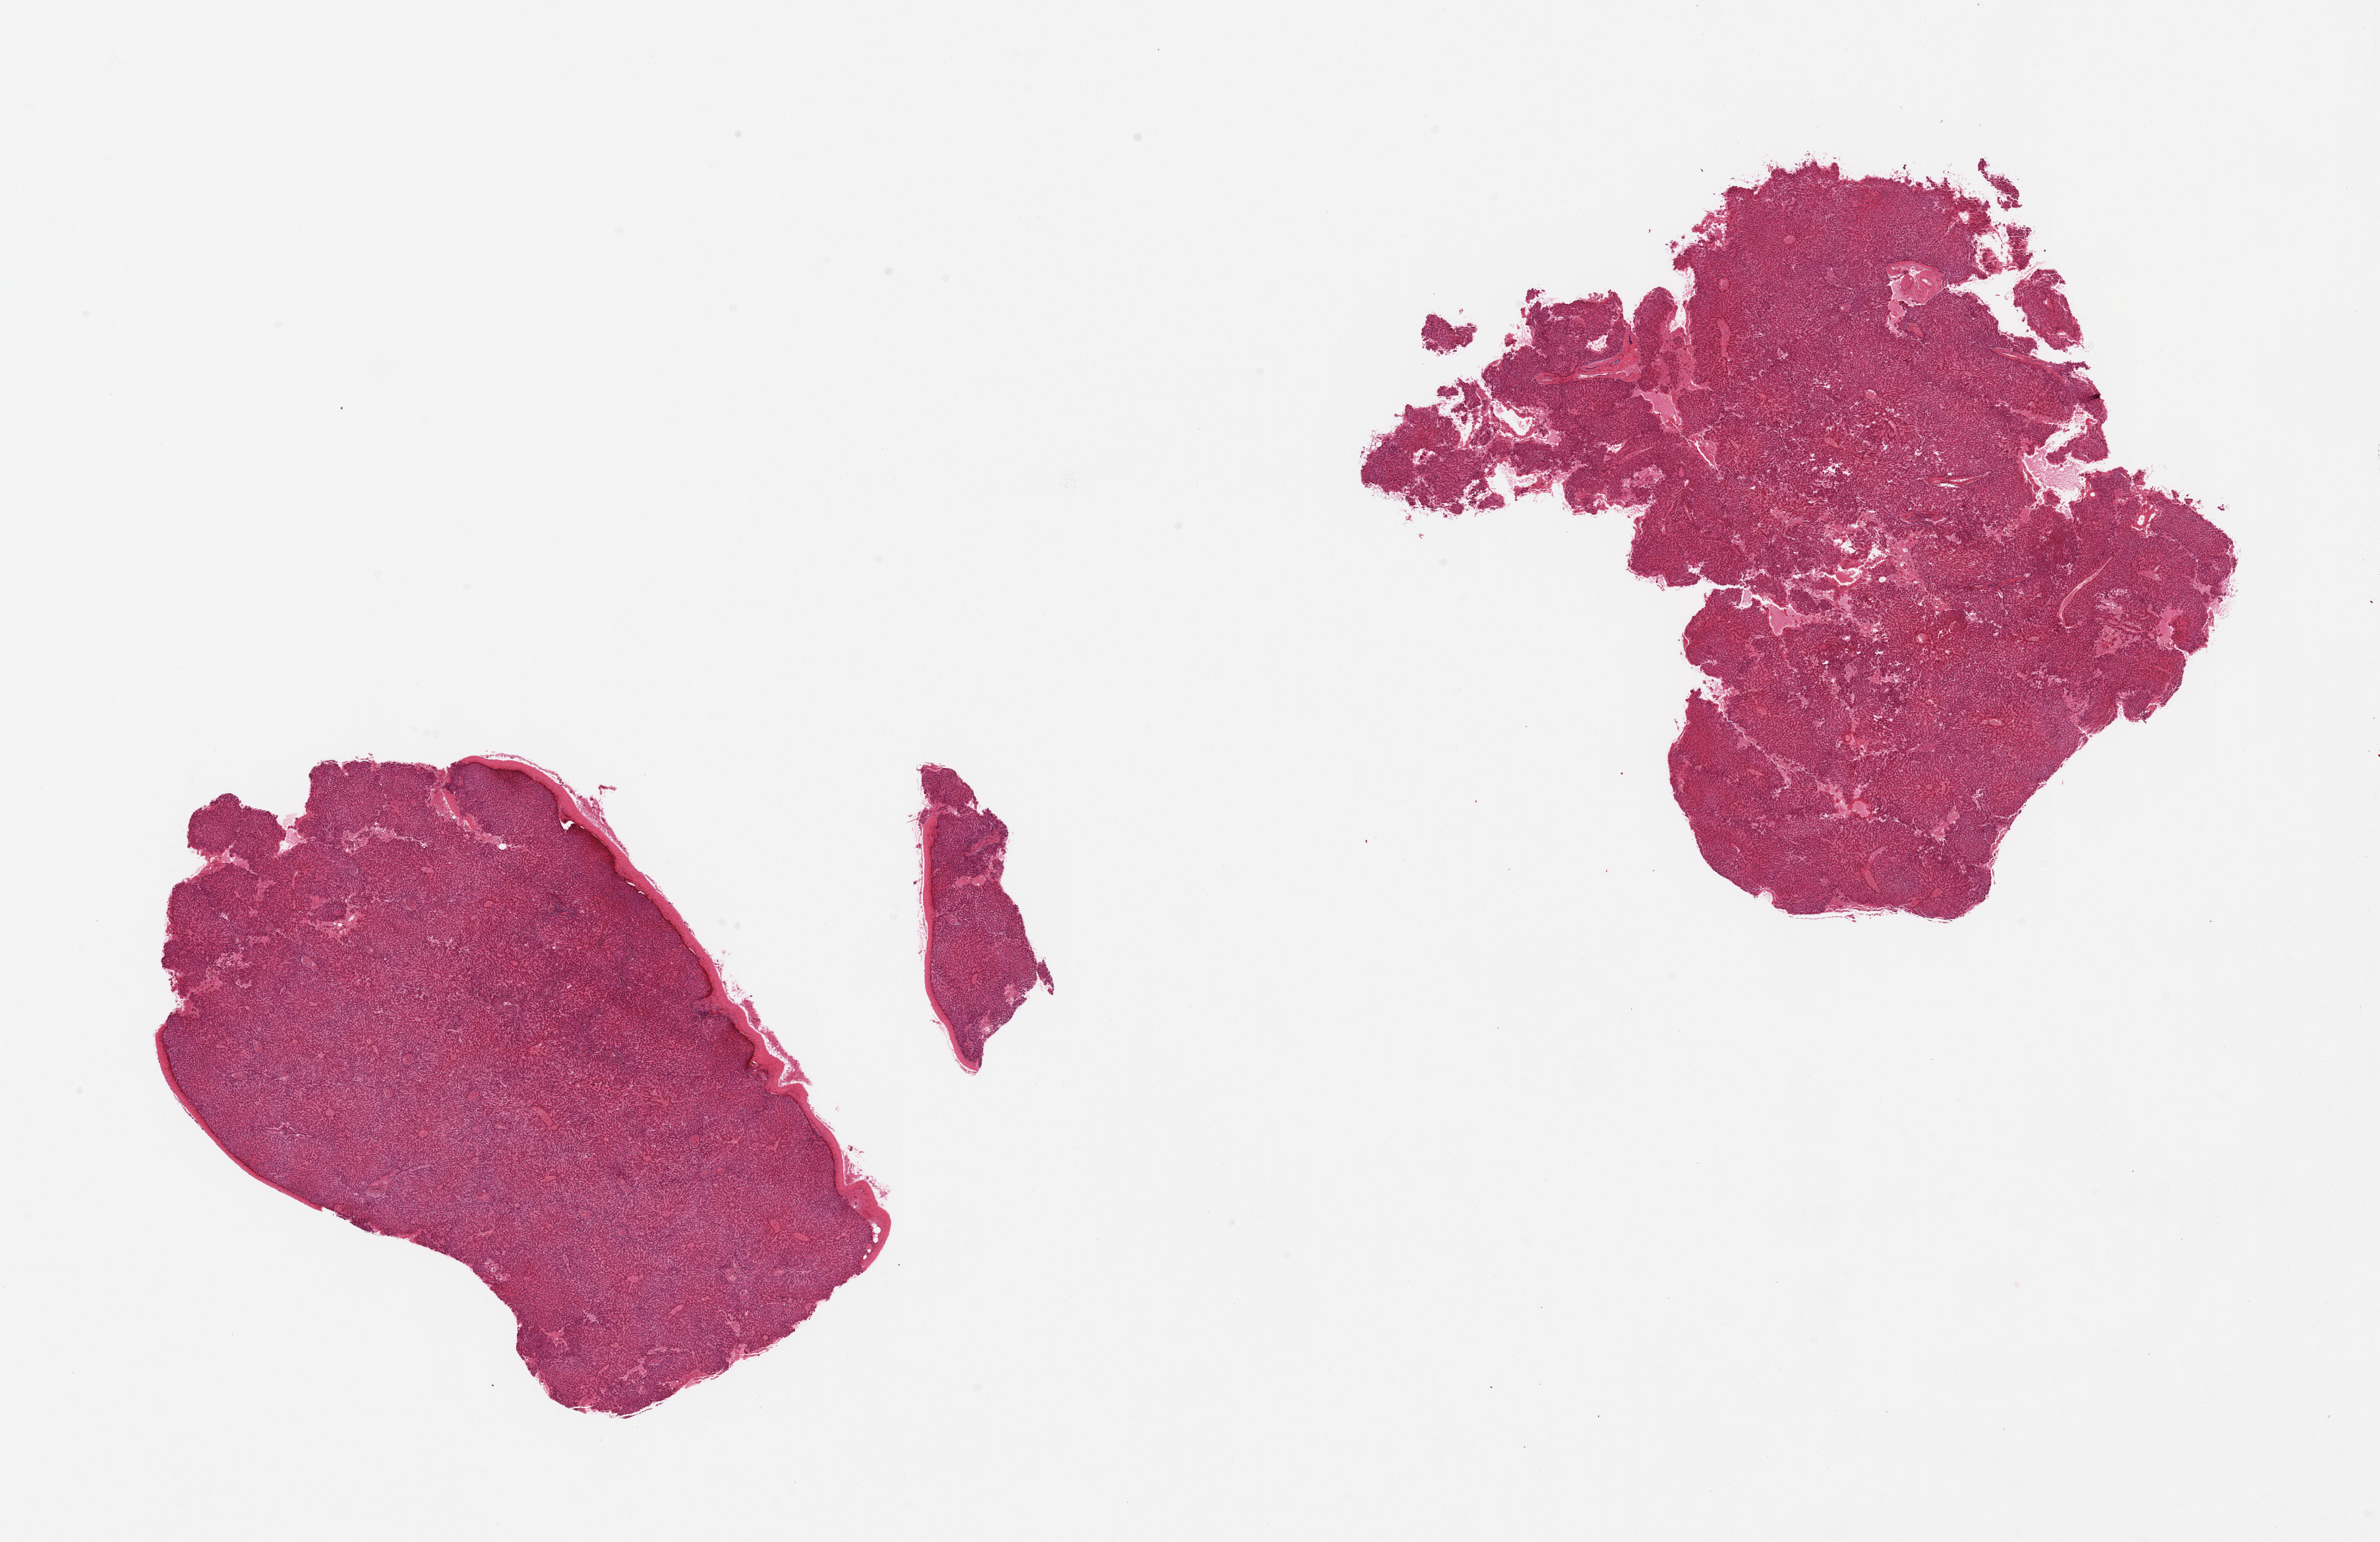
H&E whole-slide image, a low-resolution overview of the entire scanned area, about 28.5 x 18.5 mm (acquisition: 20x scan), PAXgene-fixed, paraffin-embedded tissue, sampled site (target tissue): liver, donor tissue sample.
Pathologist's review note for this sample: 2 pieces, includes capsule (target is 1 cm below capsule), few collections of lymphocytes, often in portal tracts.